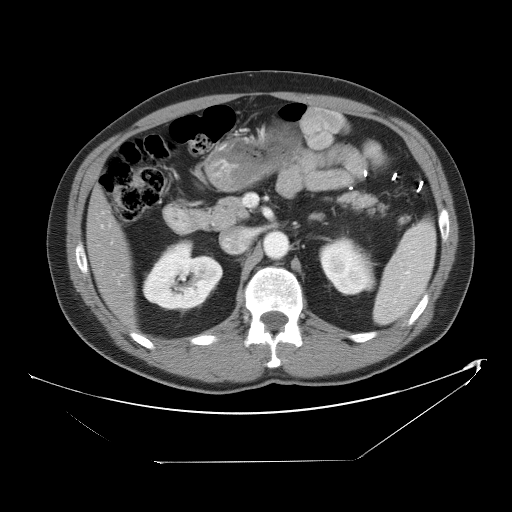
Contrast-enhanced abdominal CT, one axial slice; slice 25 of 53 in the series (ordered by position); 120 kVp; intravenous contrast given; soft-tissue window (W 400 / L 40 HU); 512 × 512 image matrix, field of view 438 × 438 mm. Male patient, age 59 years. Case-level facts recorded for this patient, not image findings: diagnosis: colorectal cancer liver metastases, imaged before liver resection; multiple liver metastases: yes; largest metastasis: 8.5 cm.
Structures marked on this image (manually delineated by an expert):
- liver: box from (x=88, y=193) to (x=136, y=326) px
- planned liver remnant (the part of the liver to remain after resection): (x=88, y=192)–(x=136, y=326)
- portal vein (with intrahepatic branches): (x=111, y=242)–(x=113, y=244)